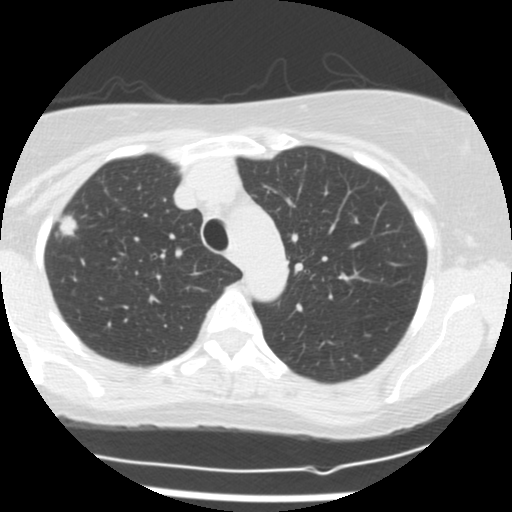
Low-dose screening chest CT, one axial slice. Reconstruction kernel STANDARD. Lung window (W 1500 / L -600 HU). 2.5 mm slice thickness. 512 × 512 image matrix, field of view 300 × 300 mm.
Annotated regions visible in this slice (manually delineated by an expert):
- lesion 1 (tumor, upper lobe of right lung): bounding box [x1, y1, x2, y2] px = [58, 215, 78, 236]